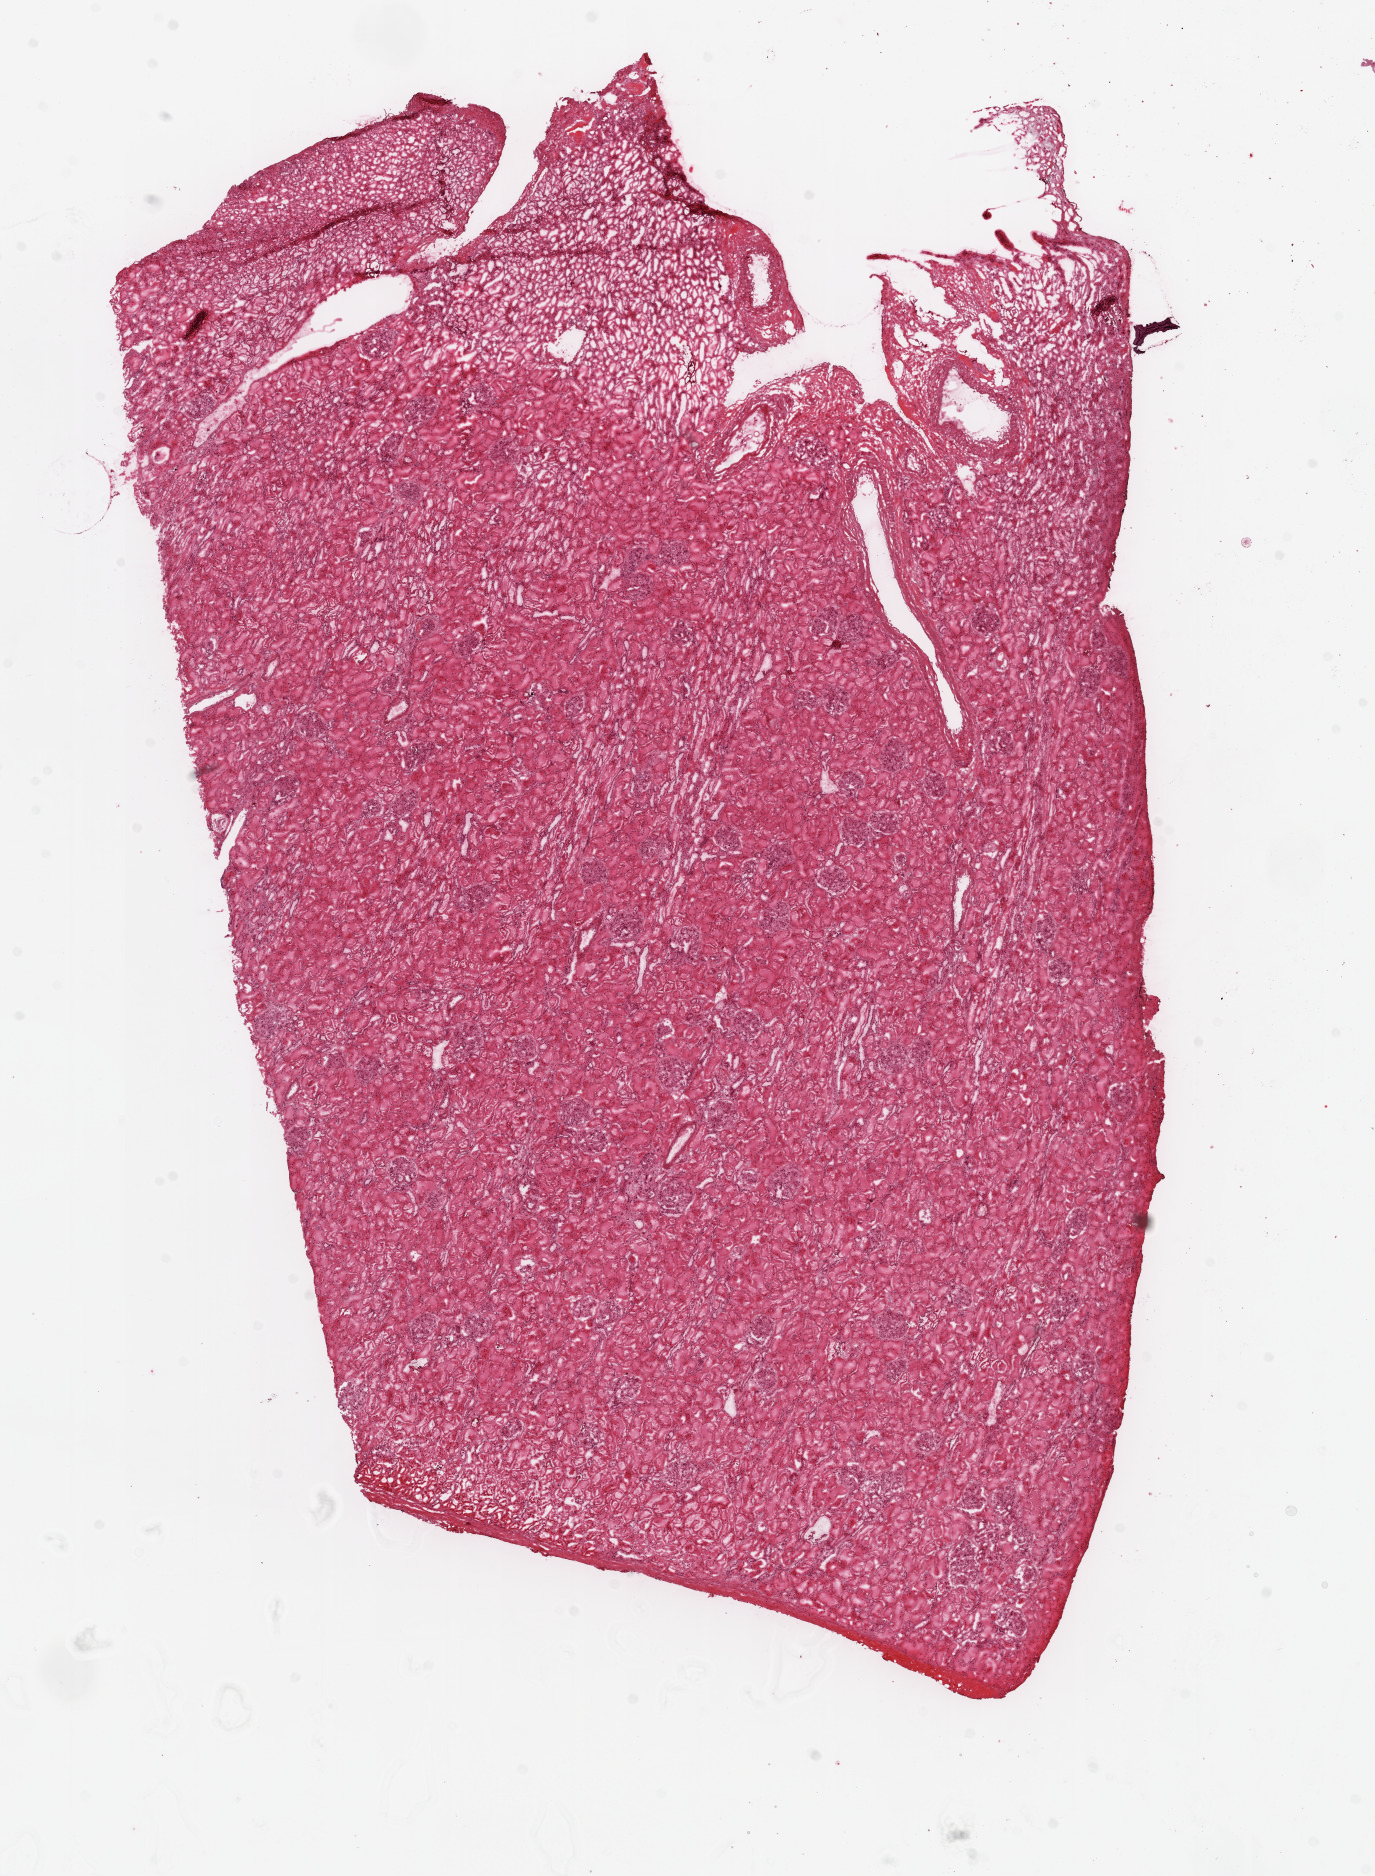
Digitized H&E tissue section (whole slide), a low-resolution overview of the entire scanned area, about 11.0 x 15.1 mm (from a 20x scan). Frozen section from the top of the tissue portion. Sample: solid tissue normal (non-tumour tissue), kidney. Male, age 58 years at initial diagnosis.
This section: solid tissue normal (non-tumour) sample from the same patient. Patient diagnosis: Clear cell adenocarcinoma, NOS.